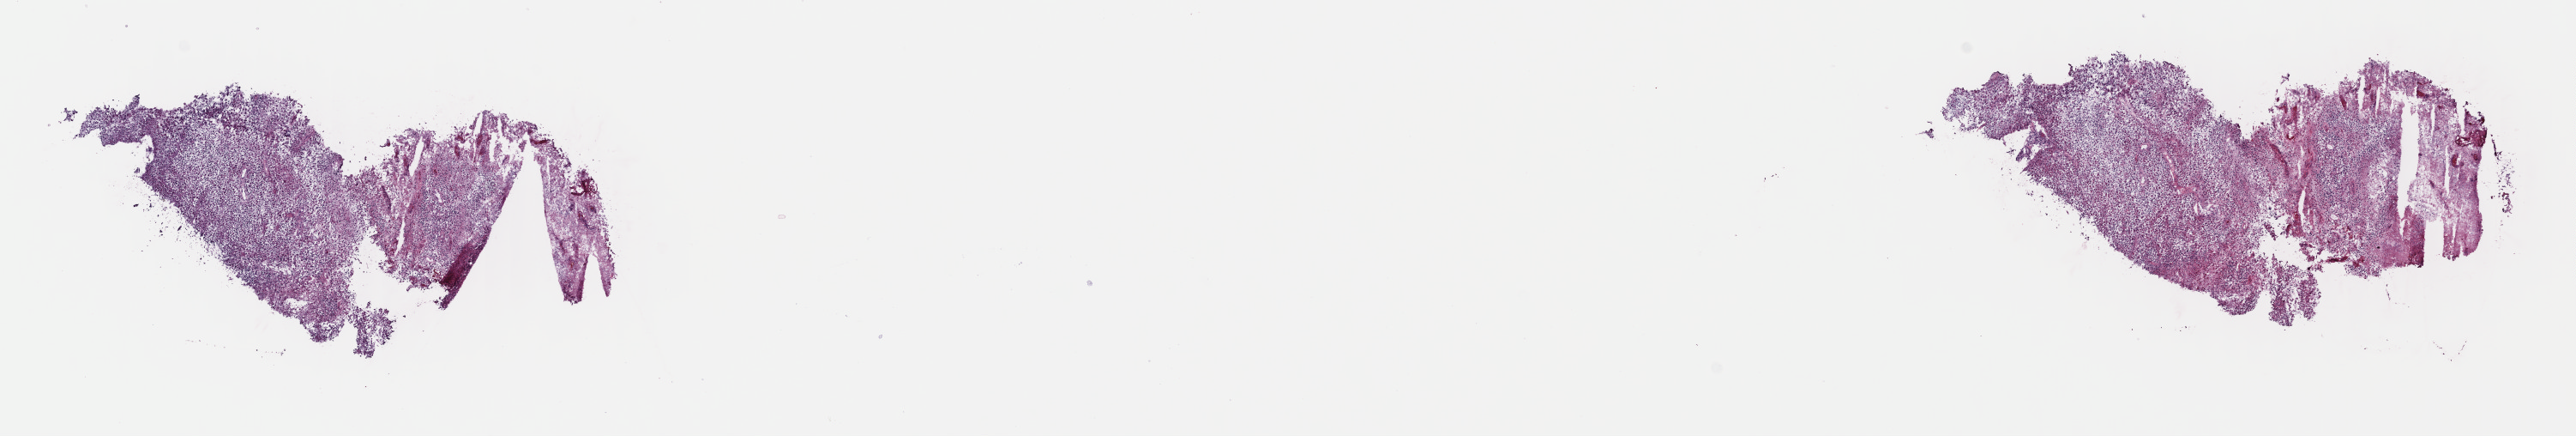
Digitized H&E-stained tissue section (whole slide), low-resolution overview of the scanned area, about 23.6 x 4.0 mm; frozen section from the top of the tissue portion; brain, primary tumour sample. Male patient; age at initial diagnosis 50 years. Slide review estimates, as recorded: tumour cells 80%, tumour nuclei 90%.
Diagnosis: Mixed glioma (cerebrum).